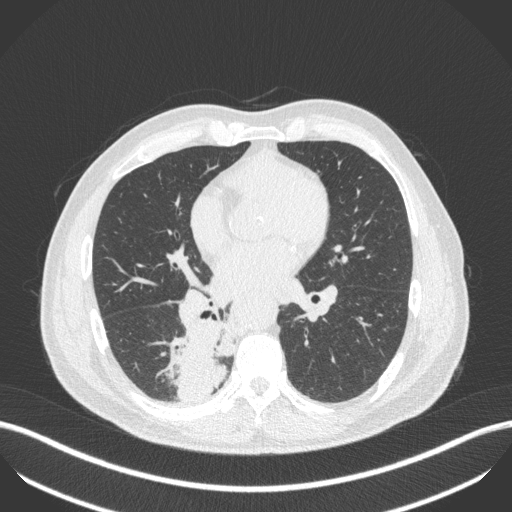
Chest CT, one axial slice; position 225 of 451 along the scan axis; reconstruction kernel B31f; lung window (W 1500 / L -600 HU); 1 mm slice thickness; 512 × 512 image matrix, field of view 400 × 400 mm. Male patient, age 61 years. Case-level facts recorded for this patient, not image findings: clinical TNM (as recorded): T1 N0 M0.
Structures marked on this image (bounding box drawn by a radiologist):
- lung tumour (recorded histology: small cell carcinoma): bounding box <179,314,230,403> (left, top, right, bottom; pixels)